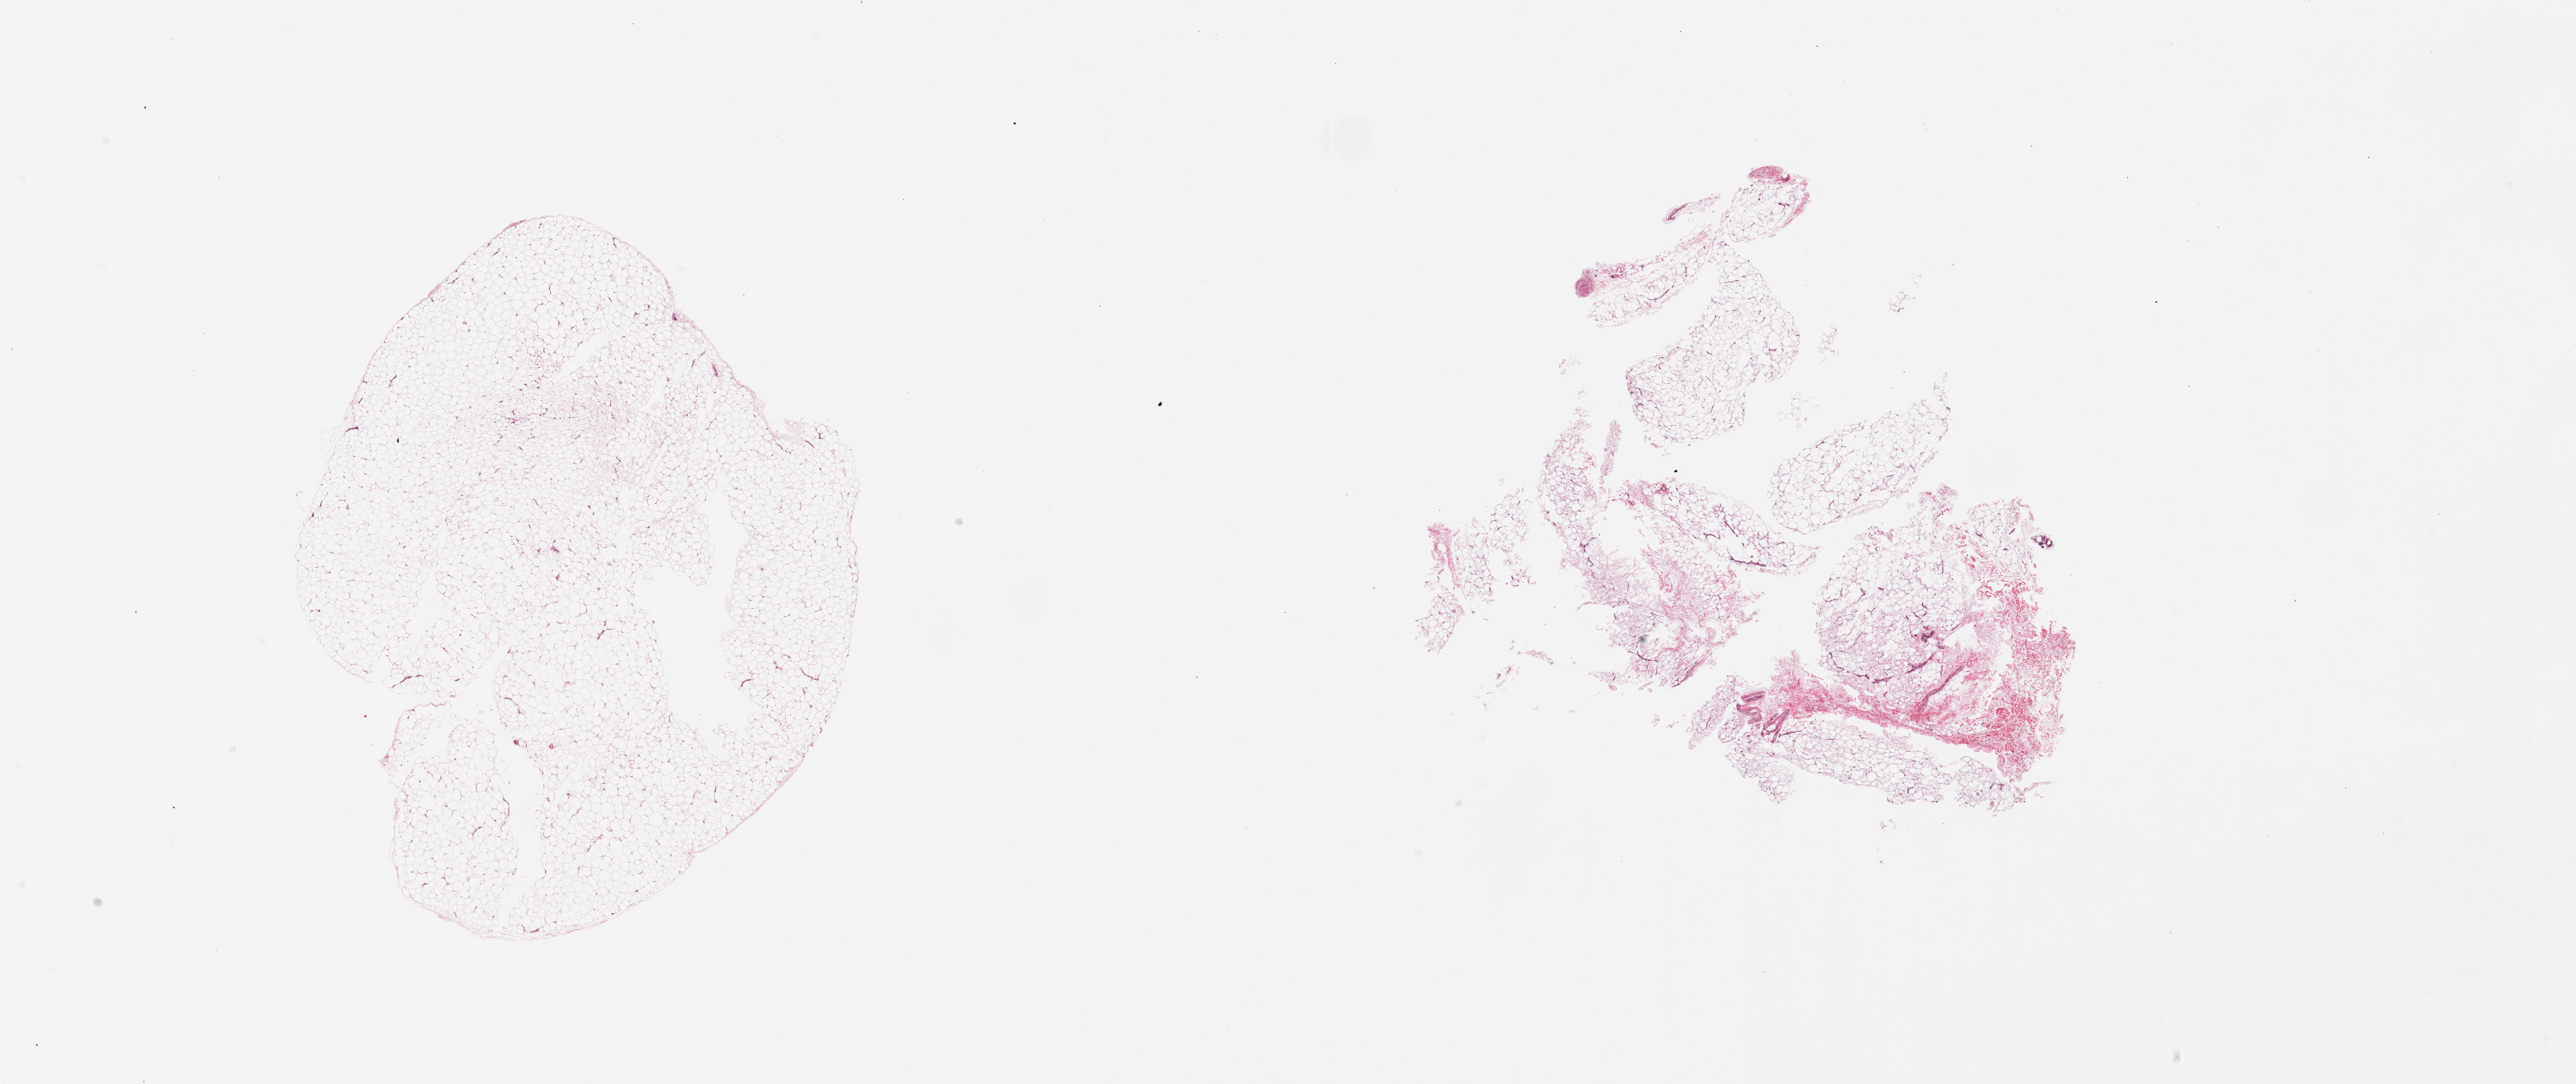
Digitized haematoxylin and eosin-stained section, whole scanned area (about 30.5 x 12.8 mm) shown as a low-resolution overview, PAXgene-fixed paraffin-embedded (PFPE) section, target tissue: adipose tissue, donor tissue sample. Donor: male.
Reviewer comment on this tissue sample: 2 pieces; one piece fragmented and contains ~10% of fibrovascular component and a few adnexal ducts.